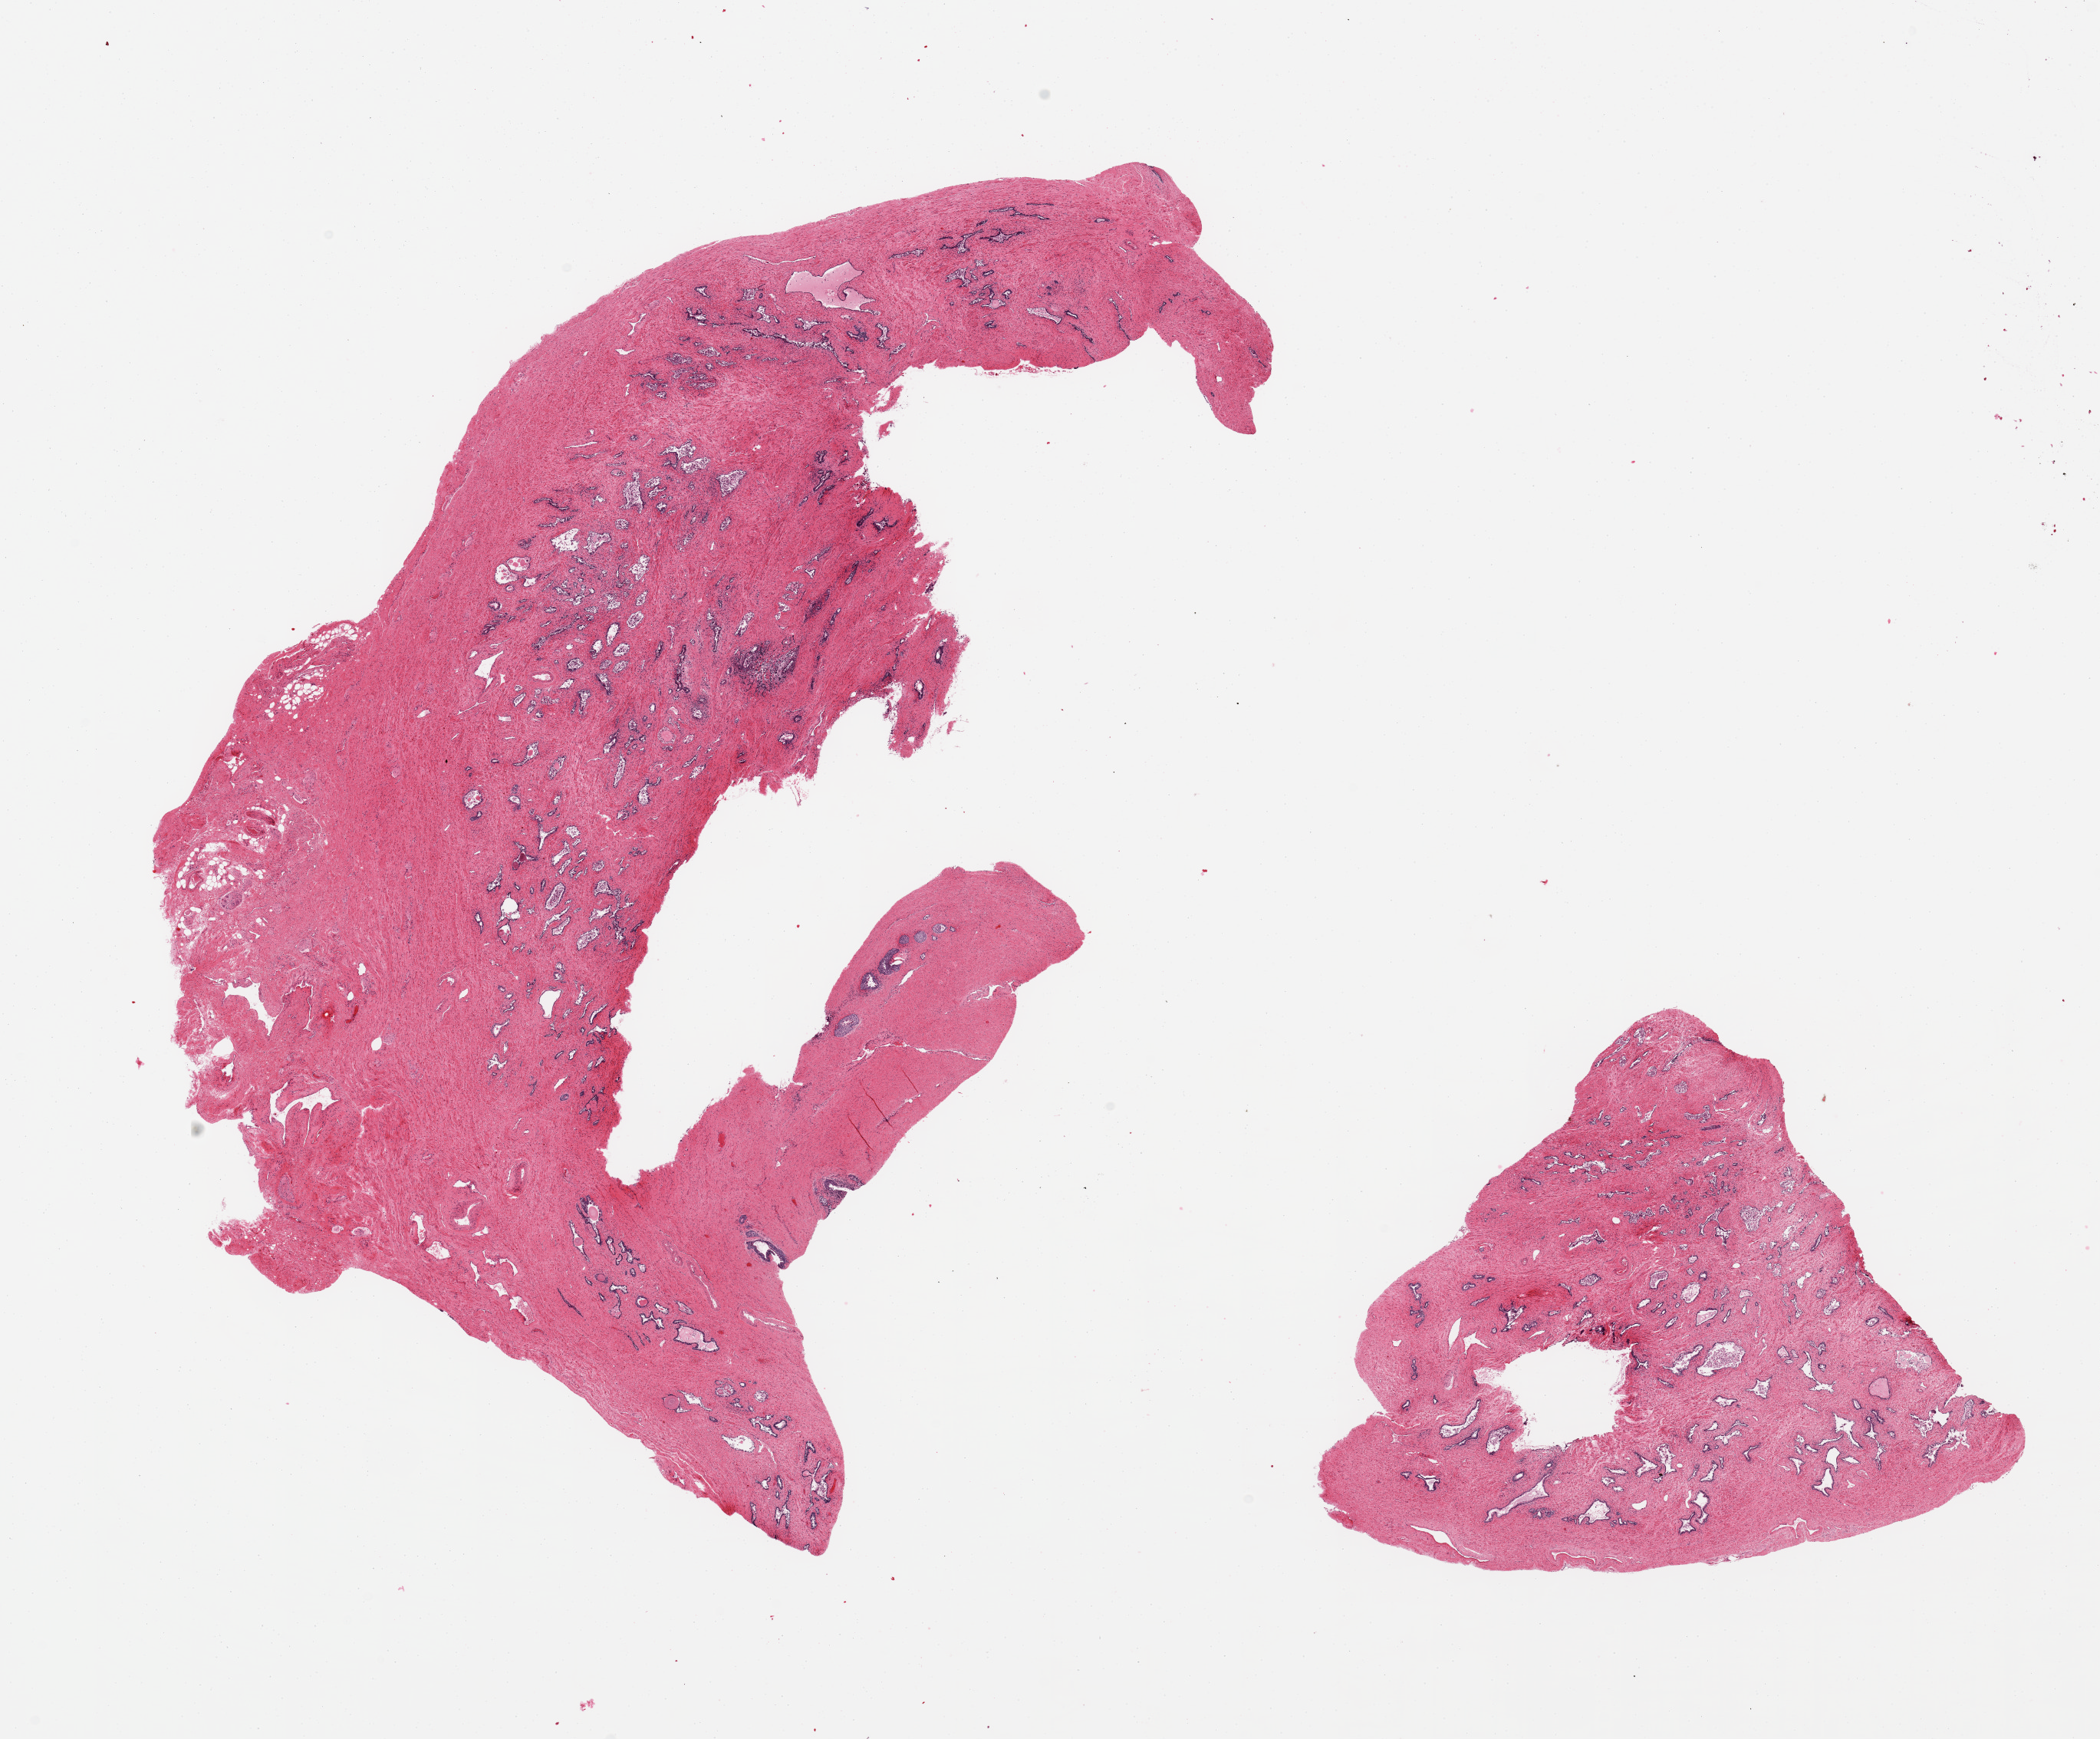
H&E whole-slide image, shown as a low-resolution overview of the whole scanned area (about 21.7 x 17.9 mm, slide scanned at 20x). PAXgene-fixed, paraffin-embedded tissue. Section of prostate (target tissue). Donor tissue sample. Donor: male.
Reviewer comment on this tissue sample: 2 pieces, glandular elements autolyzed.